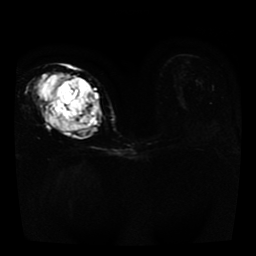
Breast MRI, one axial slice; position 21 of 41 along the scan axis; diffusion-weighted series; image 2 of 4 stored at this slice position (different b-values; order by instance number); 1.5 T; 256 × 256 image matrix, field of view 330 × 330 mm. Female patient.
Structures marked on this image (outlined manually by an expert reader):
- tumour on diffusion-weighted imaging: bounding box [x1, y1, x2, y2] px = [40, 74, 88, 134]